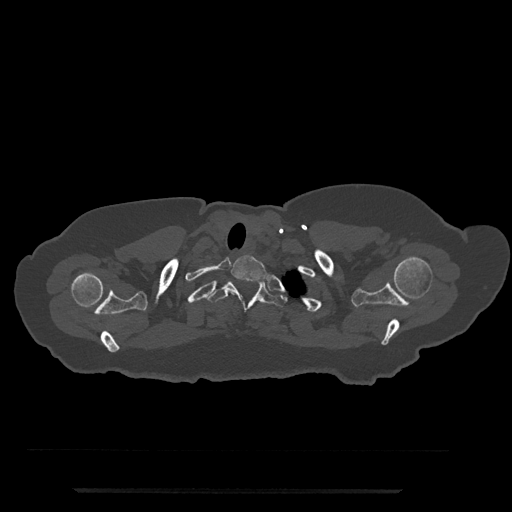
CT including the spine, one axial slice. Slice 688 of 797 in the series (ordered by position). Reconstruction kernel Br40s/3. 120 kVp. Bone window (W 1800 / L 400 HU). 512 × 512 image matrix. Female patient, age 51 years. Case-level facts recorded for this patient, not image findings: primary cancer: neuro.
Outlined on this slice (semi-automatic segmentation, software-assisted and operator-edited):
- T1 vertebra: bounding box (x1, y1, x2, y2) in pixels: (231, 255, 267, 295)
- T2 vertebra: (206, 281, 286, 313)